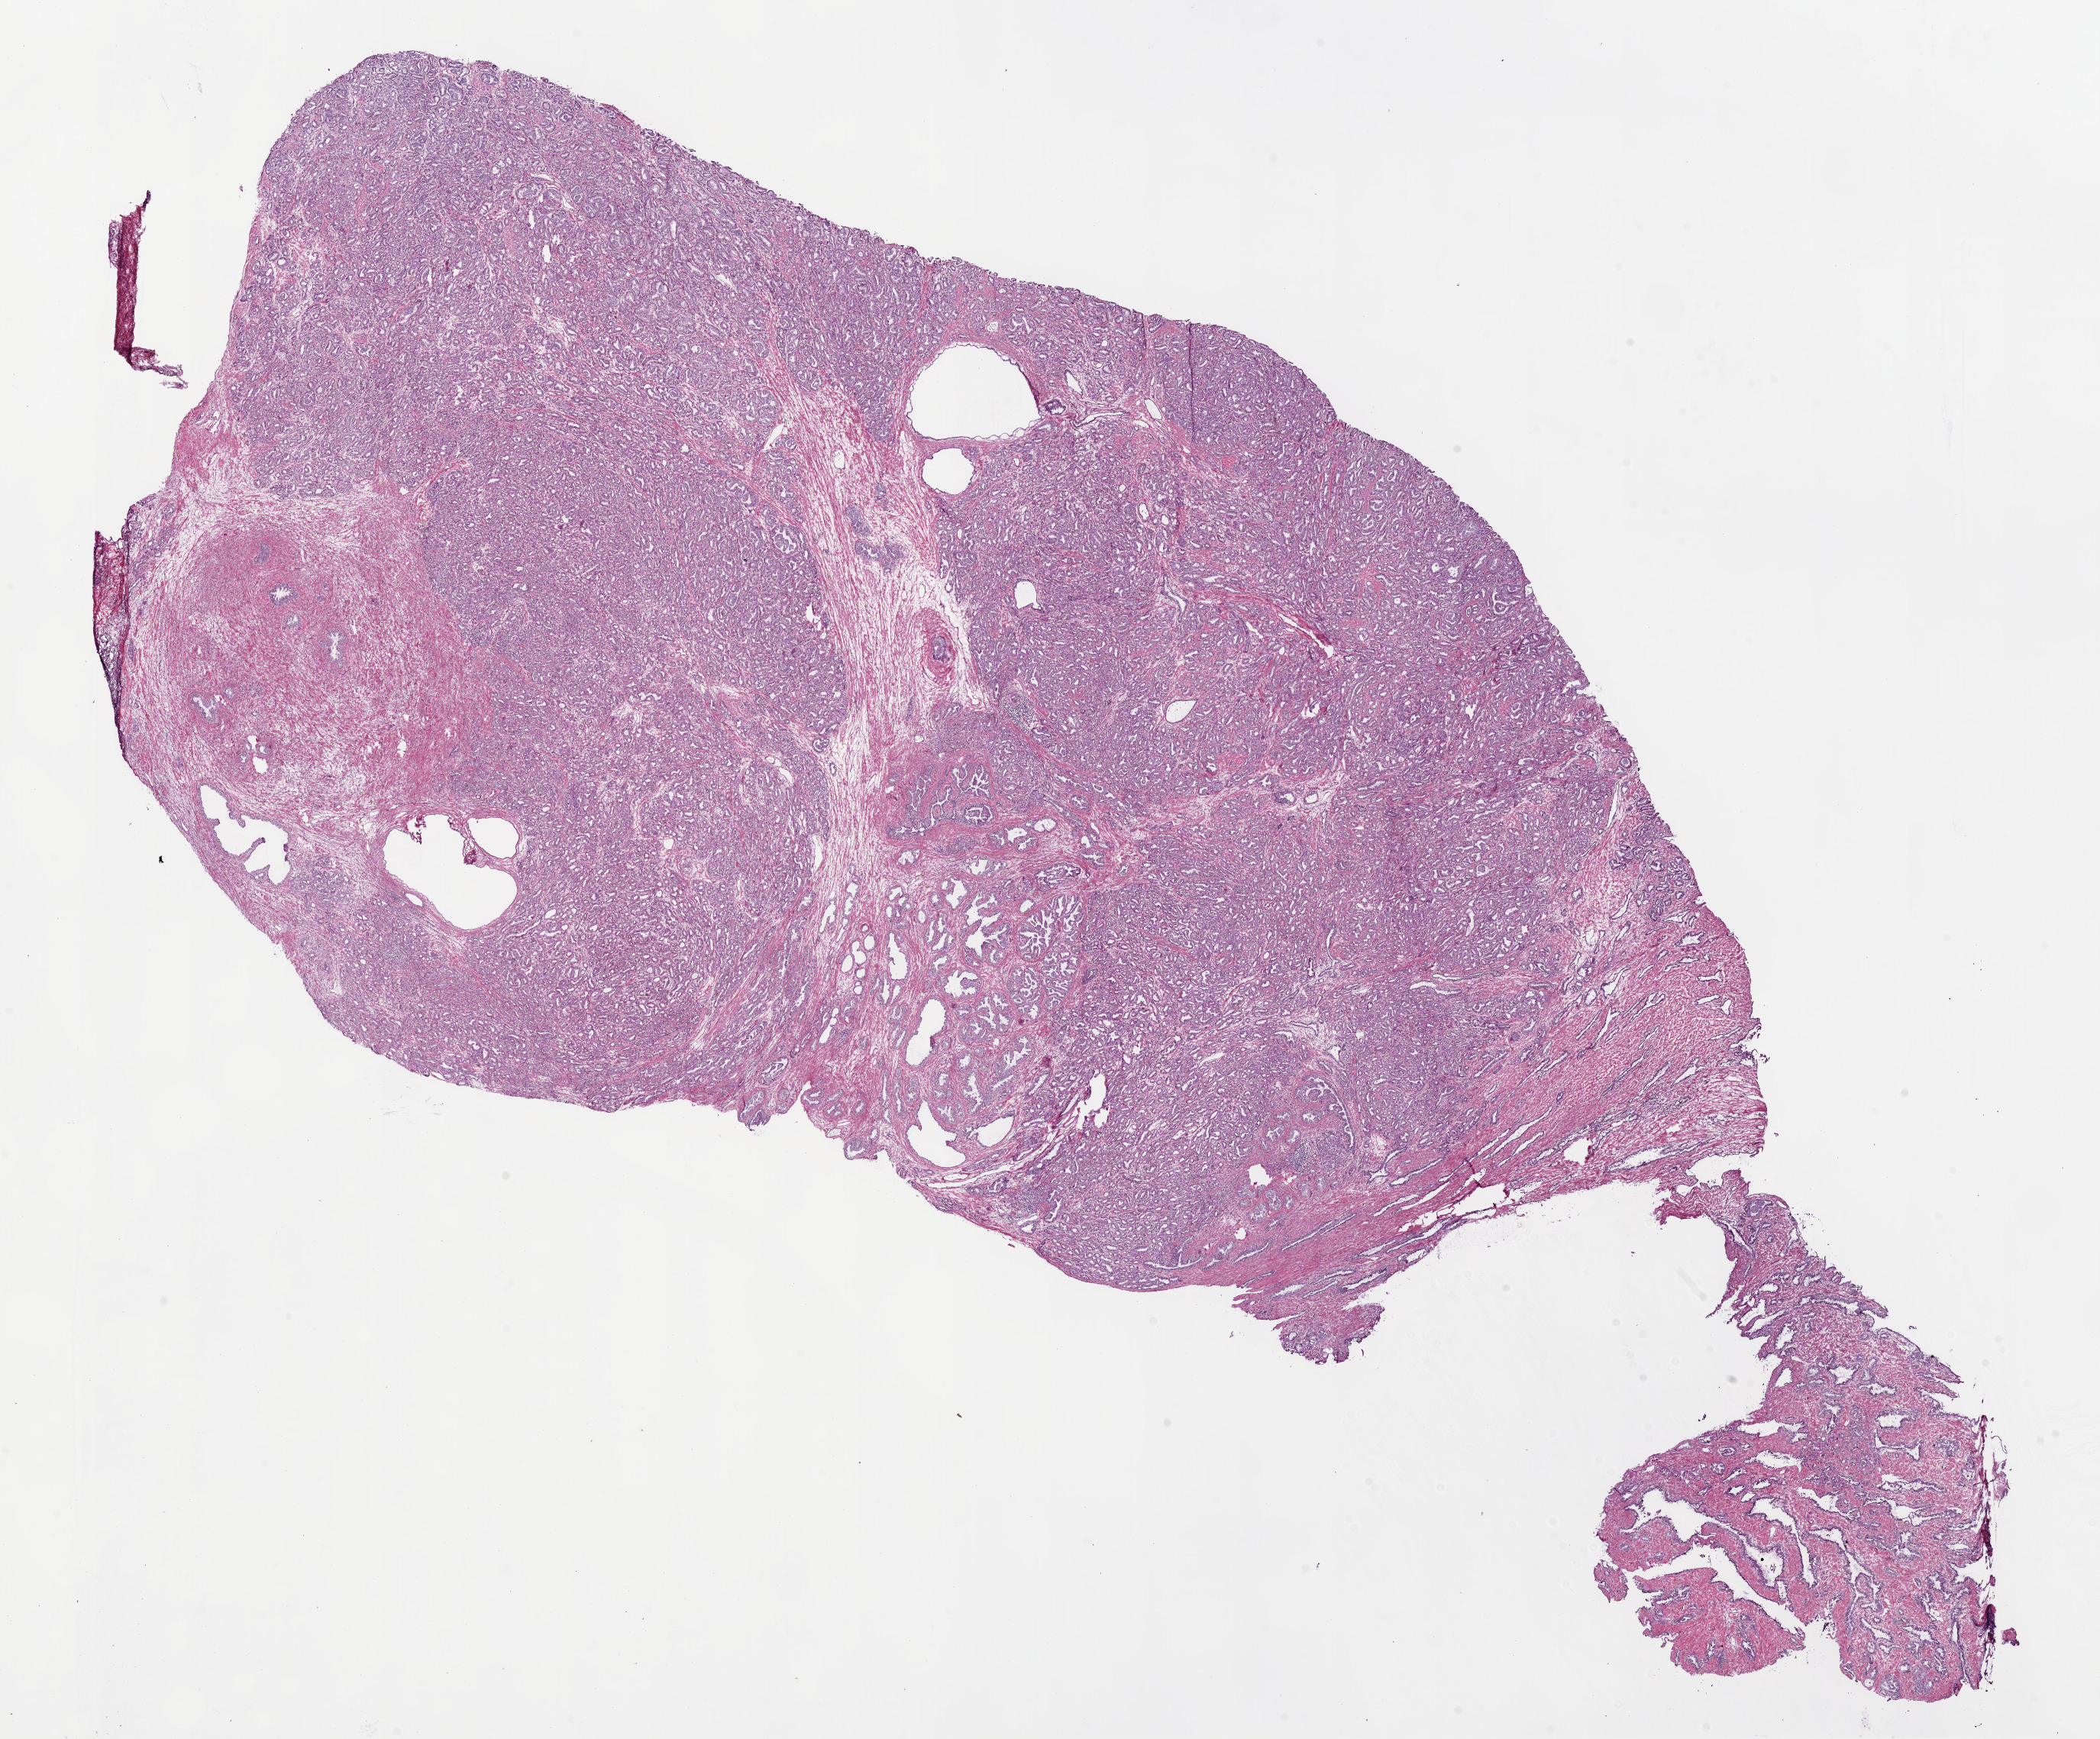
Whole-slide histology image, Hematoxylin and eosin (H&E) stained — low-resolution overview of the scanned area, about 22.1 x 18.3 mm (from a 20x scan), frozen section, sample: primary tumour, prostate. Male patient; age at initial diagnosis 57 years. Gleason score: 7 (3+4). Pathologist review of this section (percent, as recorded): tumour cells 70%, tumour nuclei 70%, normal cells 10%, stromal cells 20%, necrosis 0%. Infiltration values recorded for this section: lymphocyte infiltration 3%, monocyte infiltration 0%, neutrophil infiltration 0%.
• diagnosis: Acinar cell carcinoma (prostate gland)
• laterality: bilateral
• lymph nodes positive (case pathology): 0 of 8 examined